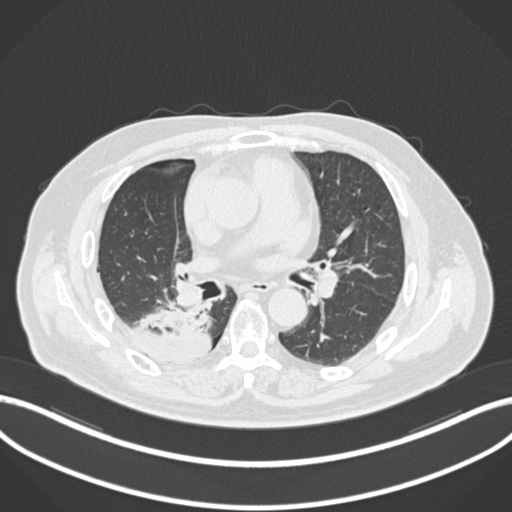
Chest CT, one axial slice. Position 99 of 218 along the scan axis. Reconstruction kernel B30f. 120 kVp. Lung window (W 1500 / L -600 HU). 512 × 512 image matrix. Male patient, age 68 years. Case-level facts recorded for this patient, not image findings: clinical TNM (as recorded): T2a N0 M0.
Annotated regions visible in this slice (rectangle marked by the reading radiologist):
- lung tumour (recorded histology: adenocarcinoma): bounding box (x1, y1, x2, y2) in pixels: (123, 297, 216, 365)